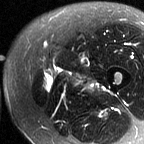
MRI of an extremity soft-tissue mass, one axial slice; slice 13 of 60 in the series (ordered by position); T2-weighted fat-saturated; MR volume resampled by the dataset authors to the PET/CT grid (not the native acquisition matrix); 3.27 mm slice thickness; 144 × 144 image matrix. Female patient. From the clinical record (not read from this slice): histological type: pleiomorphic leiomyosarcoma; grade: intermediate; site of the primary tumour: left thigh.
Outlined on this slice (expert contour drawn on MRI and transferred to this co-registered scan by the dataset authors):
- gross tumour volume including surrounding oedema: bounding box (x1, y1, x2, y2) in pixels: (45, 72, 101, 93)